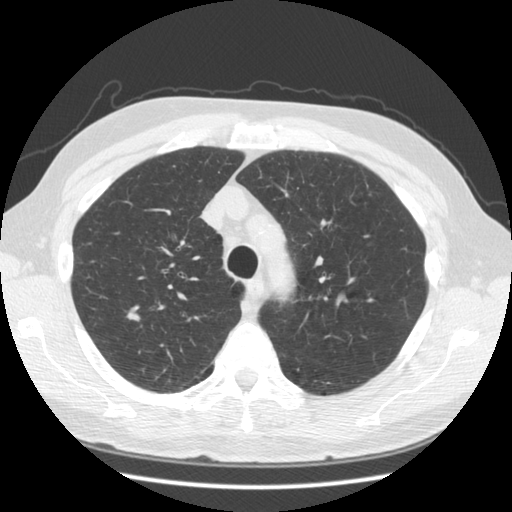
Chest CT (low-dose screening protocol), one axial image. Second annual screen. Lung window (W 1500 / L -600 HU). Standard (soft-tissue) reconstruction kernel (STANDARD). 140 kVp. Slice 117 of 155 in the series. Male, age 68 years at enrolment. Current smoker at enrolment.
Lesion marked by an expert reader, bounding box (x1, y1, x2, y2) in pixels: (108, 296, 156, 338). No non-calcified nodule or mass ≥4 mm was recorded by the screening reader at this exam. Official screen result: negative screen, minor abnormalities not suspicious for lung cancer. Later outcome: lung cancer diagnosed 596 days after this screen (after the third annual screen) — adenocarcinoma, NOS, right upper lobe, moderately differentiated (G2), stage IA (AJCC 6th edition), 13 mm at pathology.